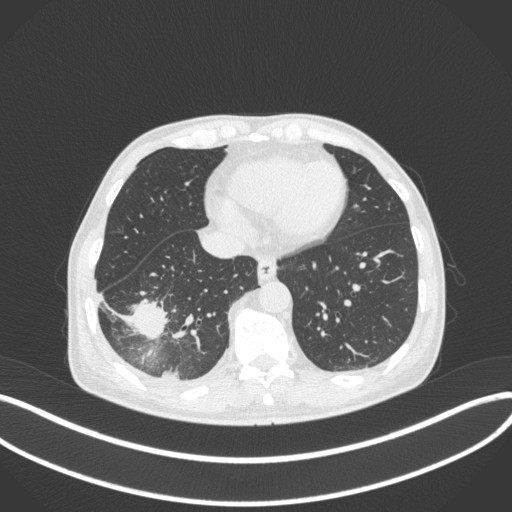
Chest CT, one axial slice. Position 108 of 385 along the scan axis. Reconstruction kernel B31f. Lung window (W 1500 / L -600 HU). 1 mm slice thickness. 512 × 512 image matrix, field of view 400 × 400 mm. Male patient, age 64 years. From the clinical record (not read from this slice): clinical TNM (as recorded): T3 N0 M0.
Structures marked on this image (bounding box drawn by a radiologist):
- lung tumour (recorded histology: adenocarcinoma): bounding box <121,297,169,342> (left, top, right, bottom; pixels)